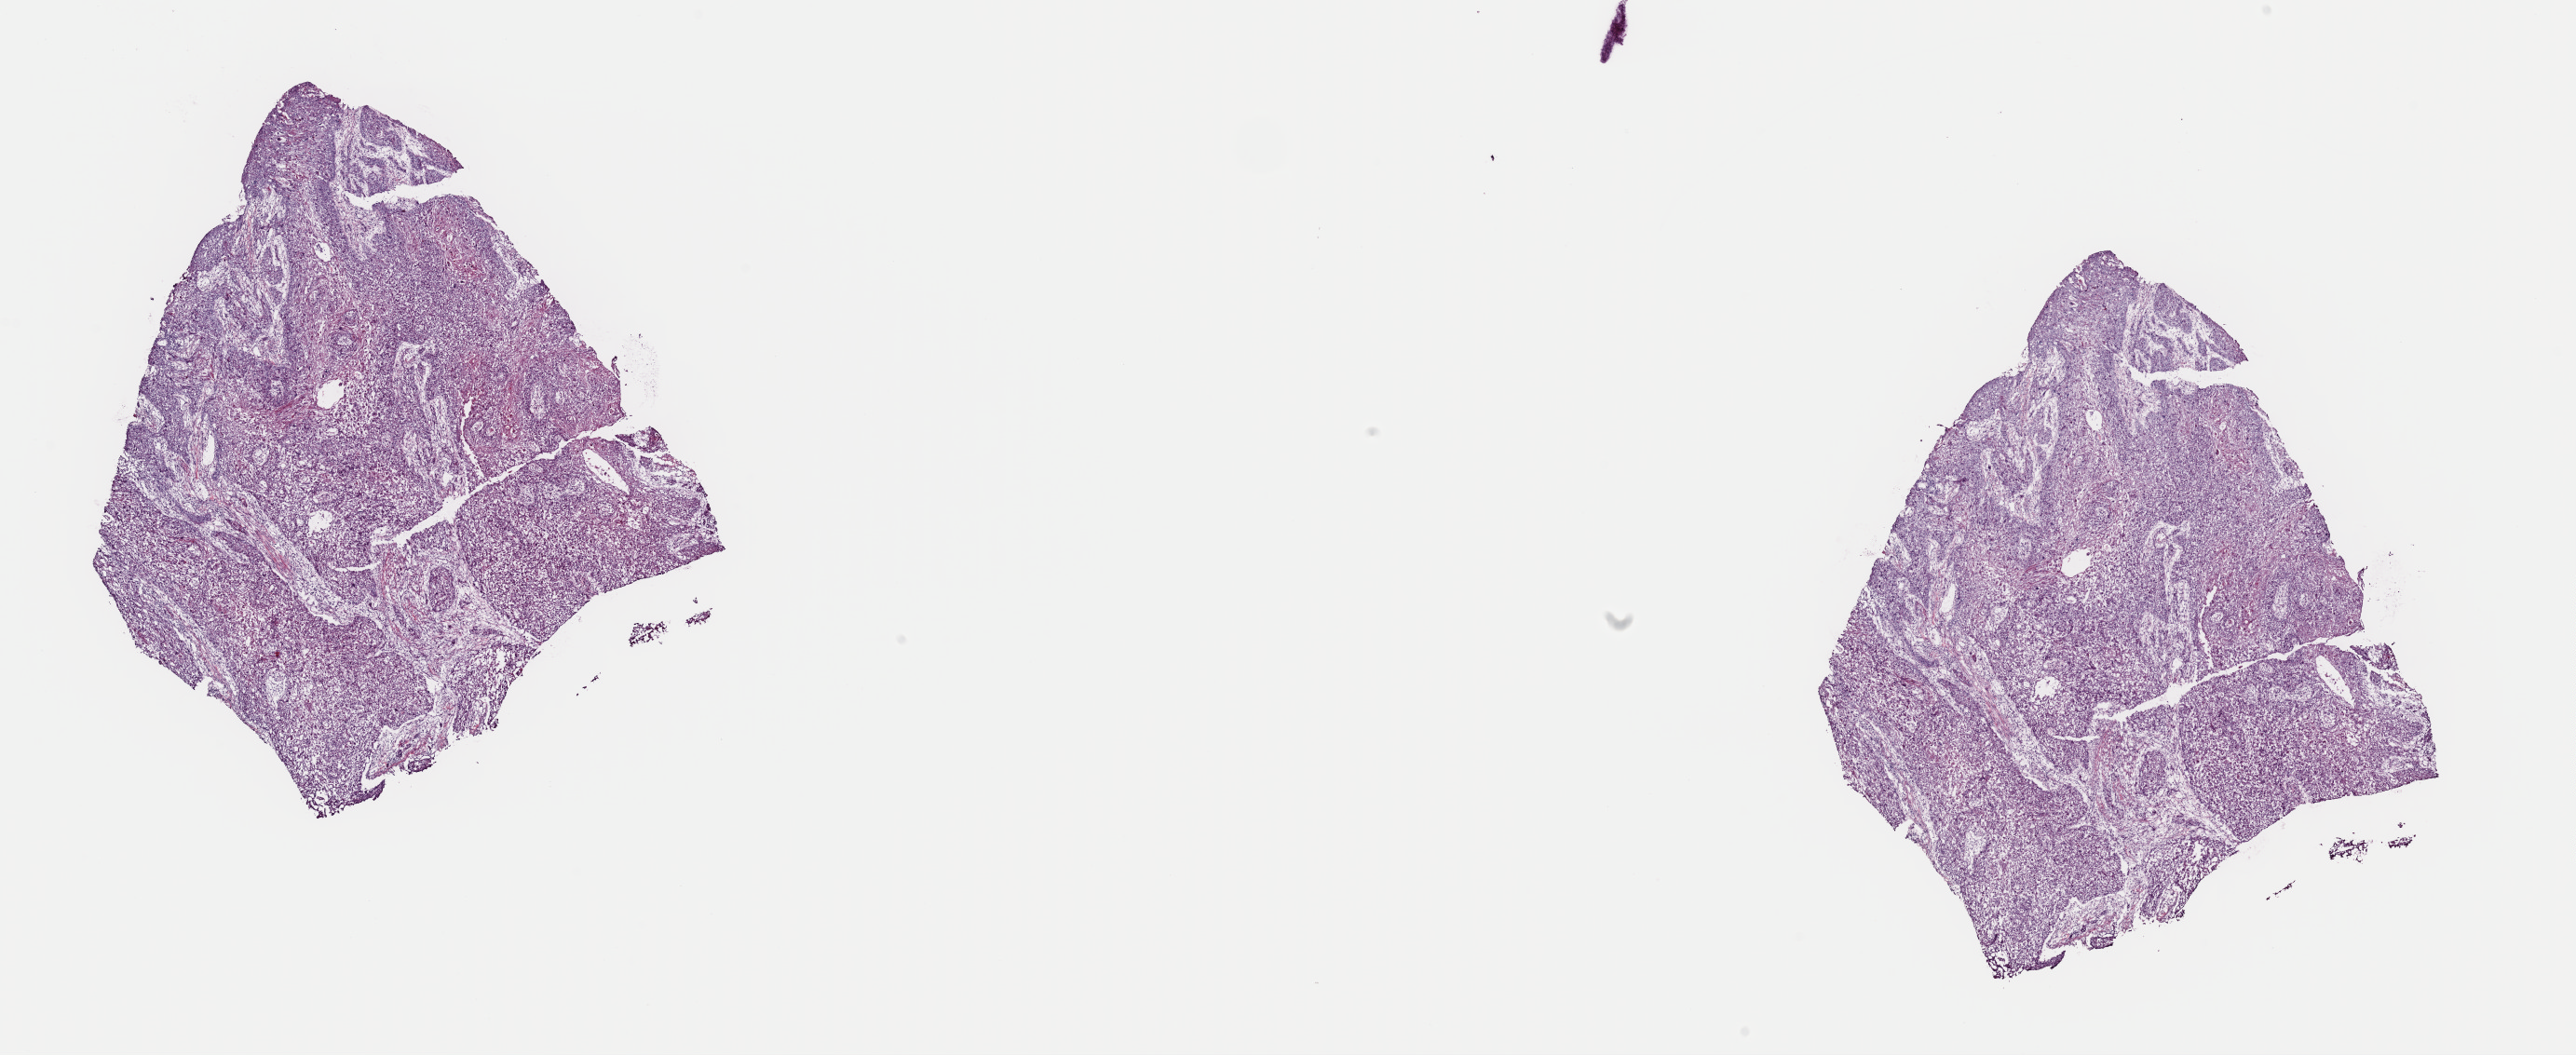
Whole-slide histology image, Hematoxylin and eosin (H&E) stained — a low-resolution overview of the entire scanned area, about 21.9 x 9.0 mm (from a 40x scan); frozen section from the top of the tissue portion; sample: primary tumour, esophagus. Female patient; age at initial diagnosis 57 years. Histologic grade: G2 (moderately differentiated). Composition of this section per pathologist review: tumour cells 100%, tumour nuclei 68%, normal cells 0%, stromal cells 0%, necrosis 0%. Inflammatory infiltration, as recorded: lymphocyte infiltration 0%, monocyte infiltration 0%, neutrophil infiltration 0%.
AJCC pathologic stage: IIIB. Histologic diagnosis: Squamous cell carcinoma, NOS.